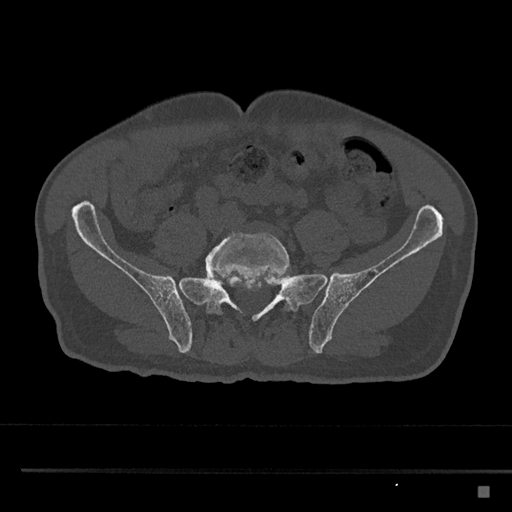
CT including the spine, one axial slice. Position 555 of 797 along the scan axis. Reconstruction kernel Br40s/3. Bone window (W 1800 / L 400 HU). 0.5 mm slice thickness. 512 × 512 image matrix. Patient: male, 59 years. Case-level facts recorded for this patient, not image findings: primary cancer: prostate.
Structures marked on this image (semi-automatically segmented with operator editing):
- L5 vertebra: bounding box <205,232,291,314> (left, top, right, bottom; pixels)